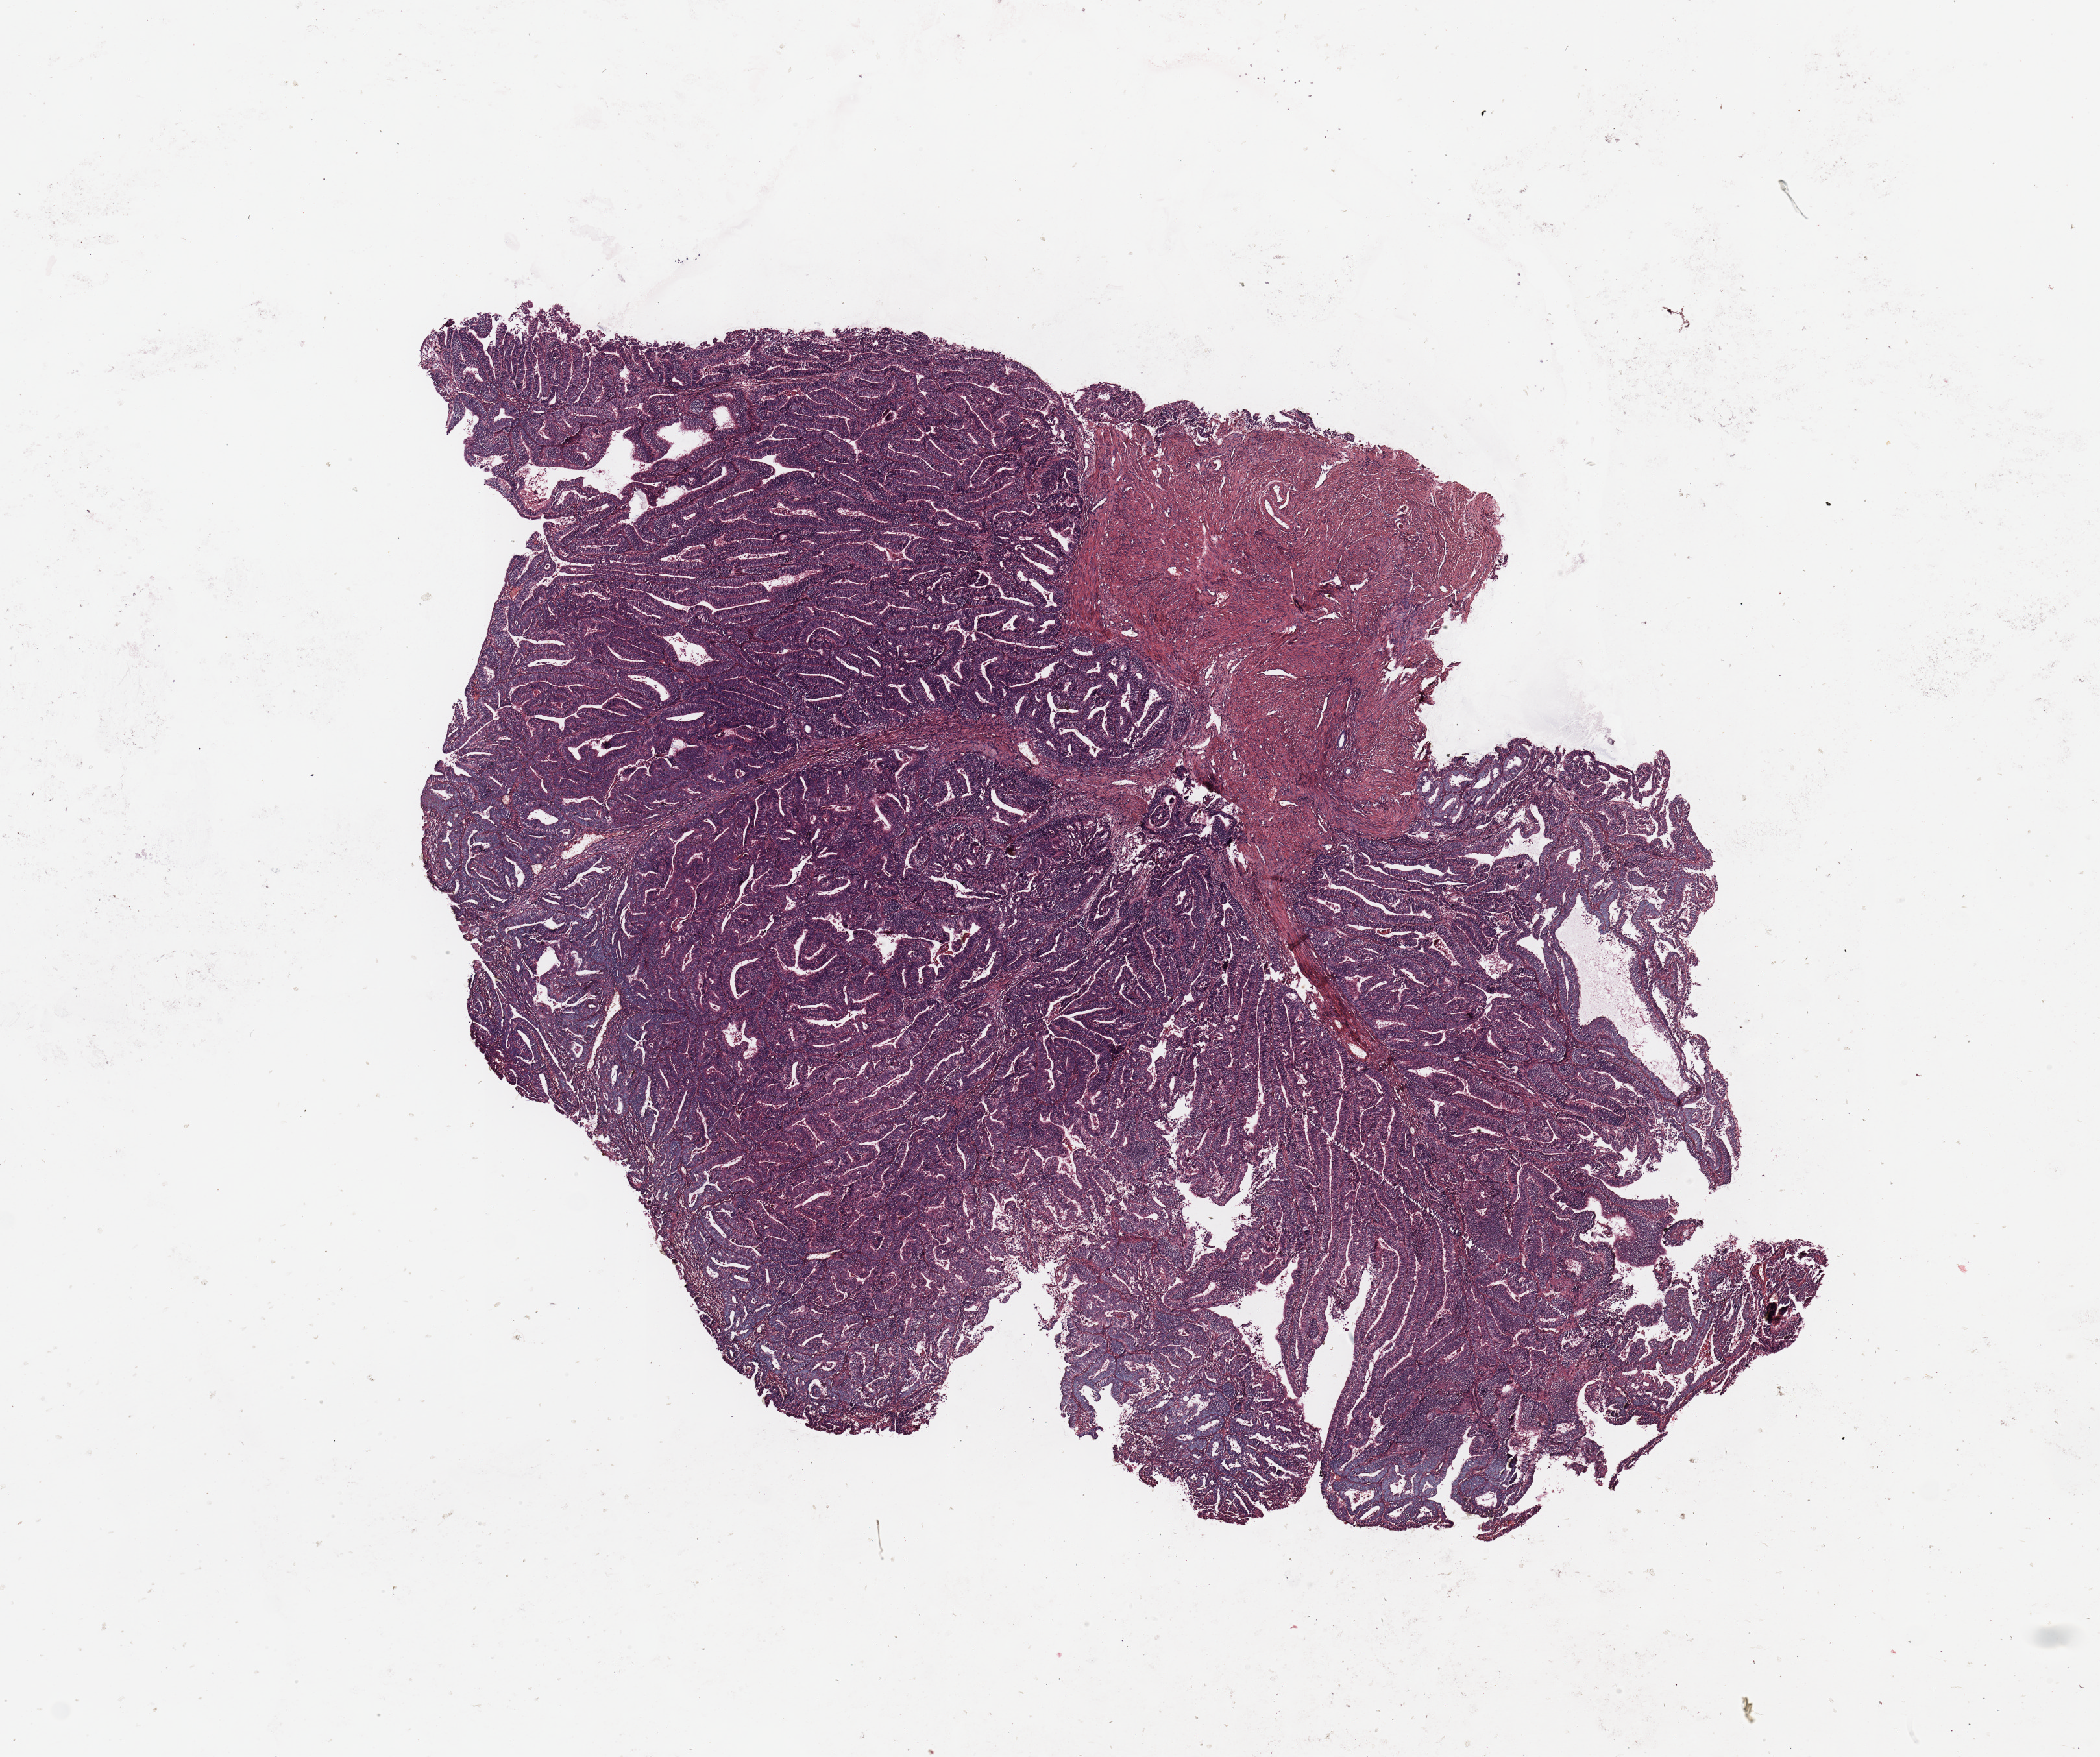
H&E whole-slide image — whole scanned area (about 12.8 x 10.7 mm) shown as a low-resolution overview. Tumour tissue sample, uterus. 66-year-old female patient. Histologic grade: G1 (well differentiated).
• AJCC pathologic stage: I
• diagnosis: Endometrioid adenocarcinoma, NOS